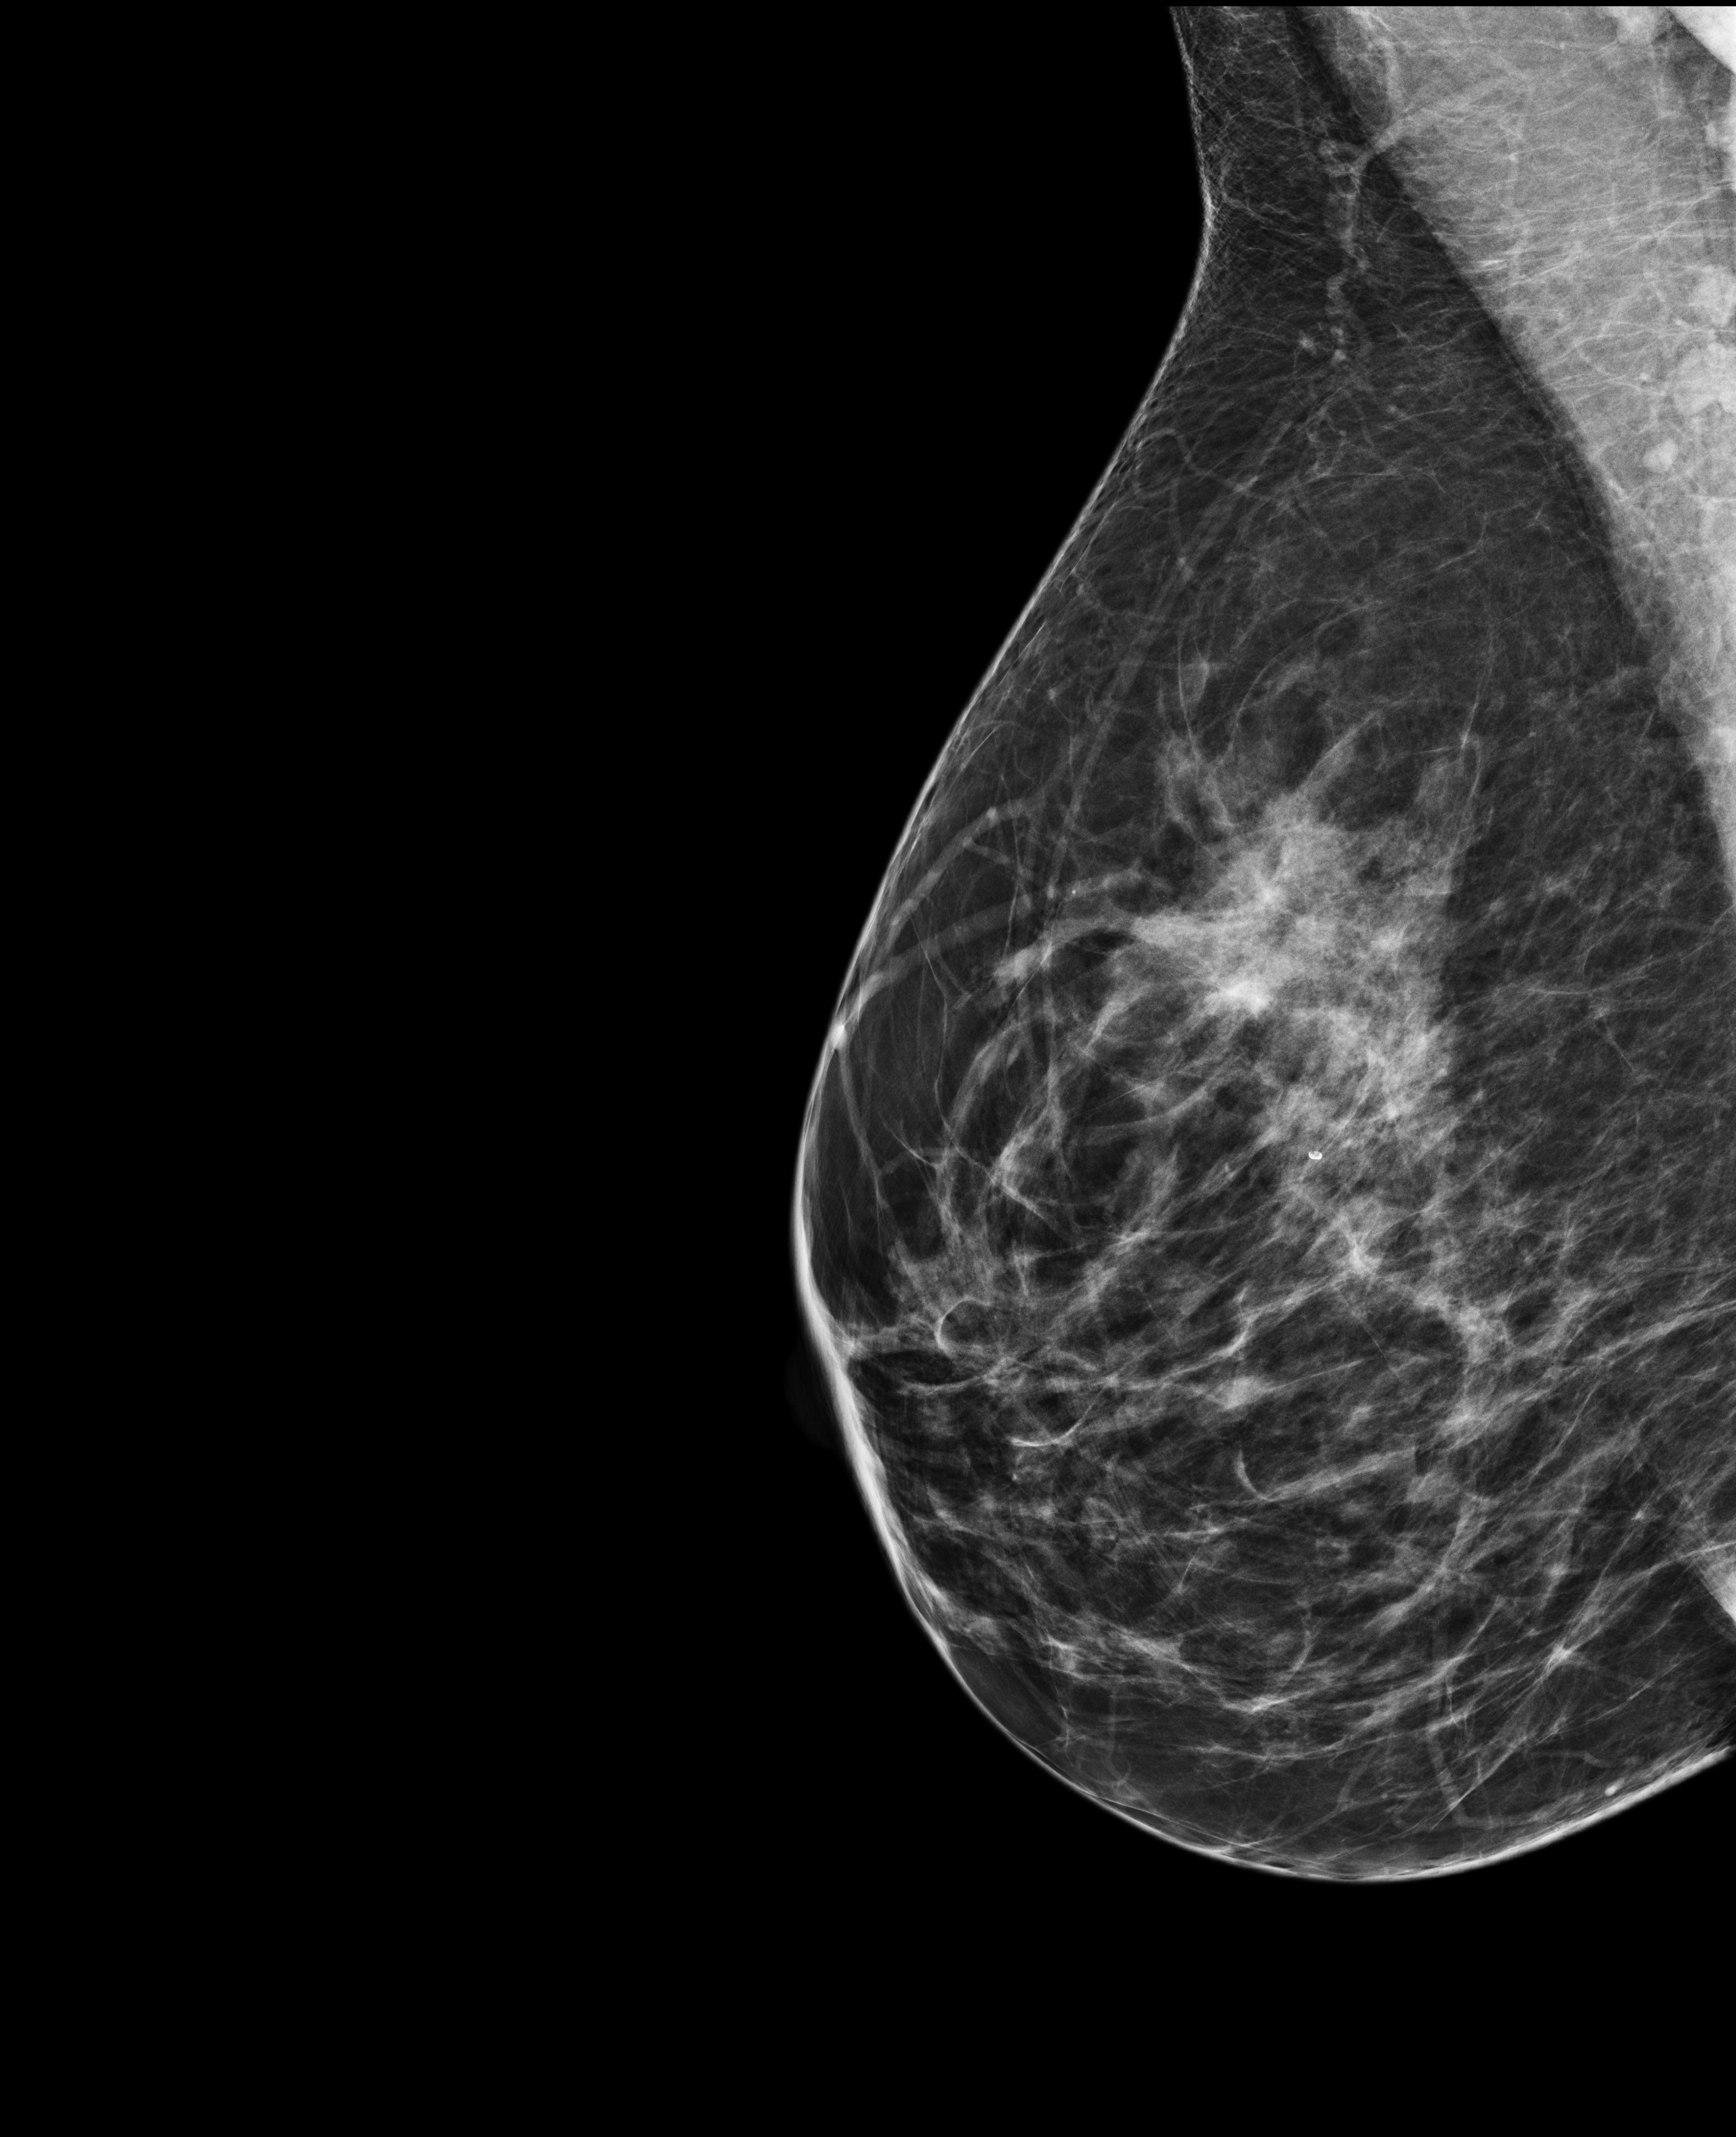
Annual screening mammography examination. Female patient, age 48 years.
Image type: full-field digital mammogram. Breast: right. Projection: medio-lateral oblique projection.